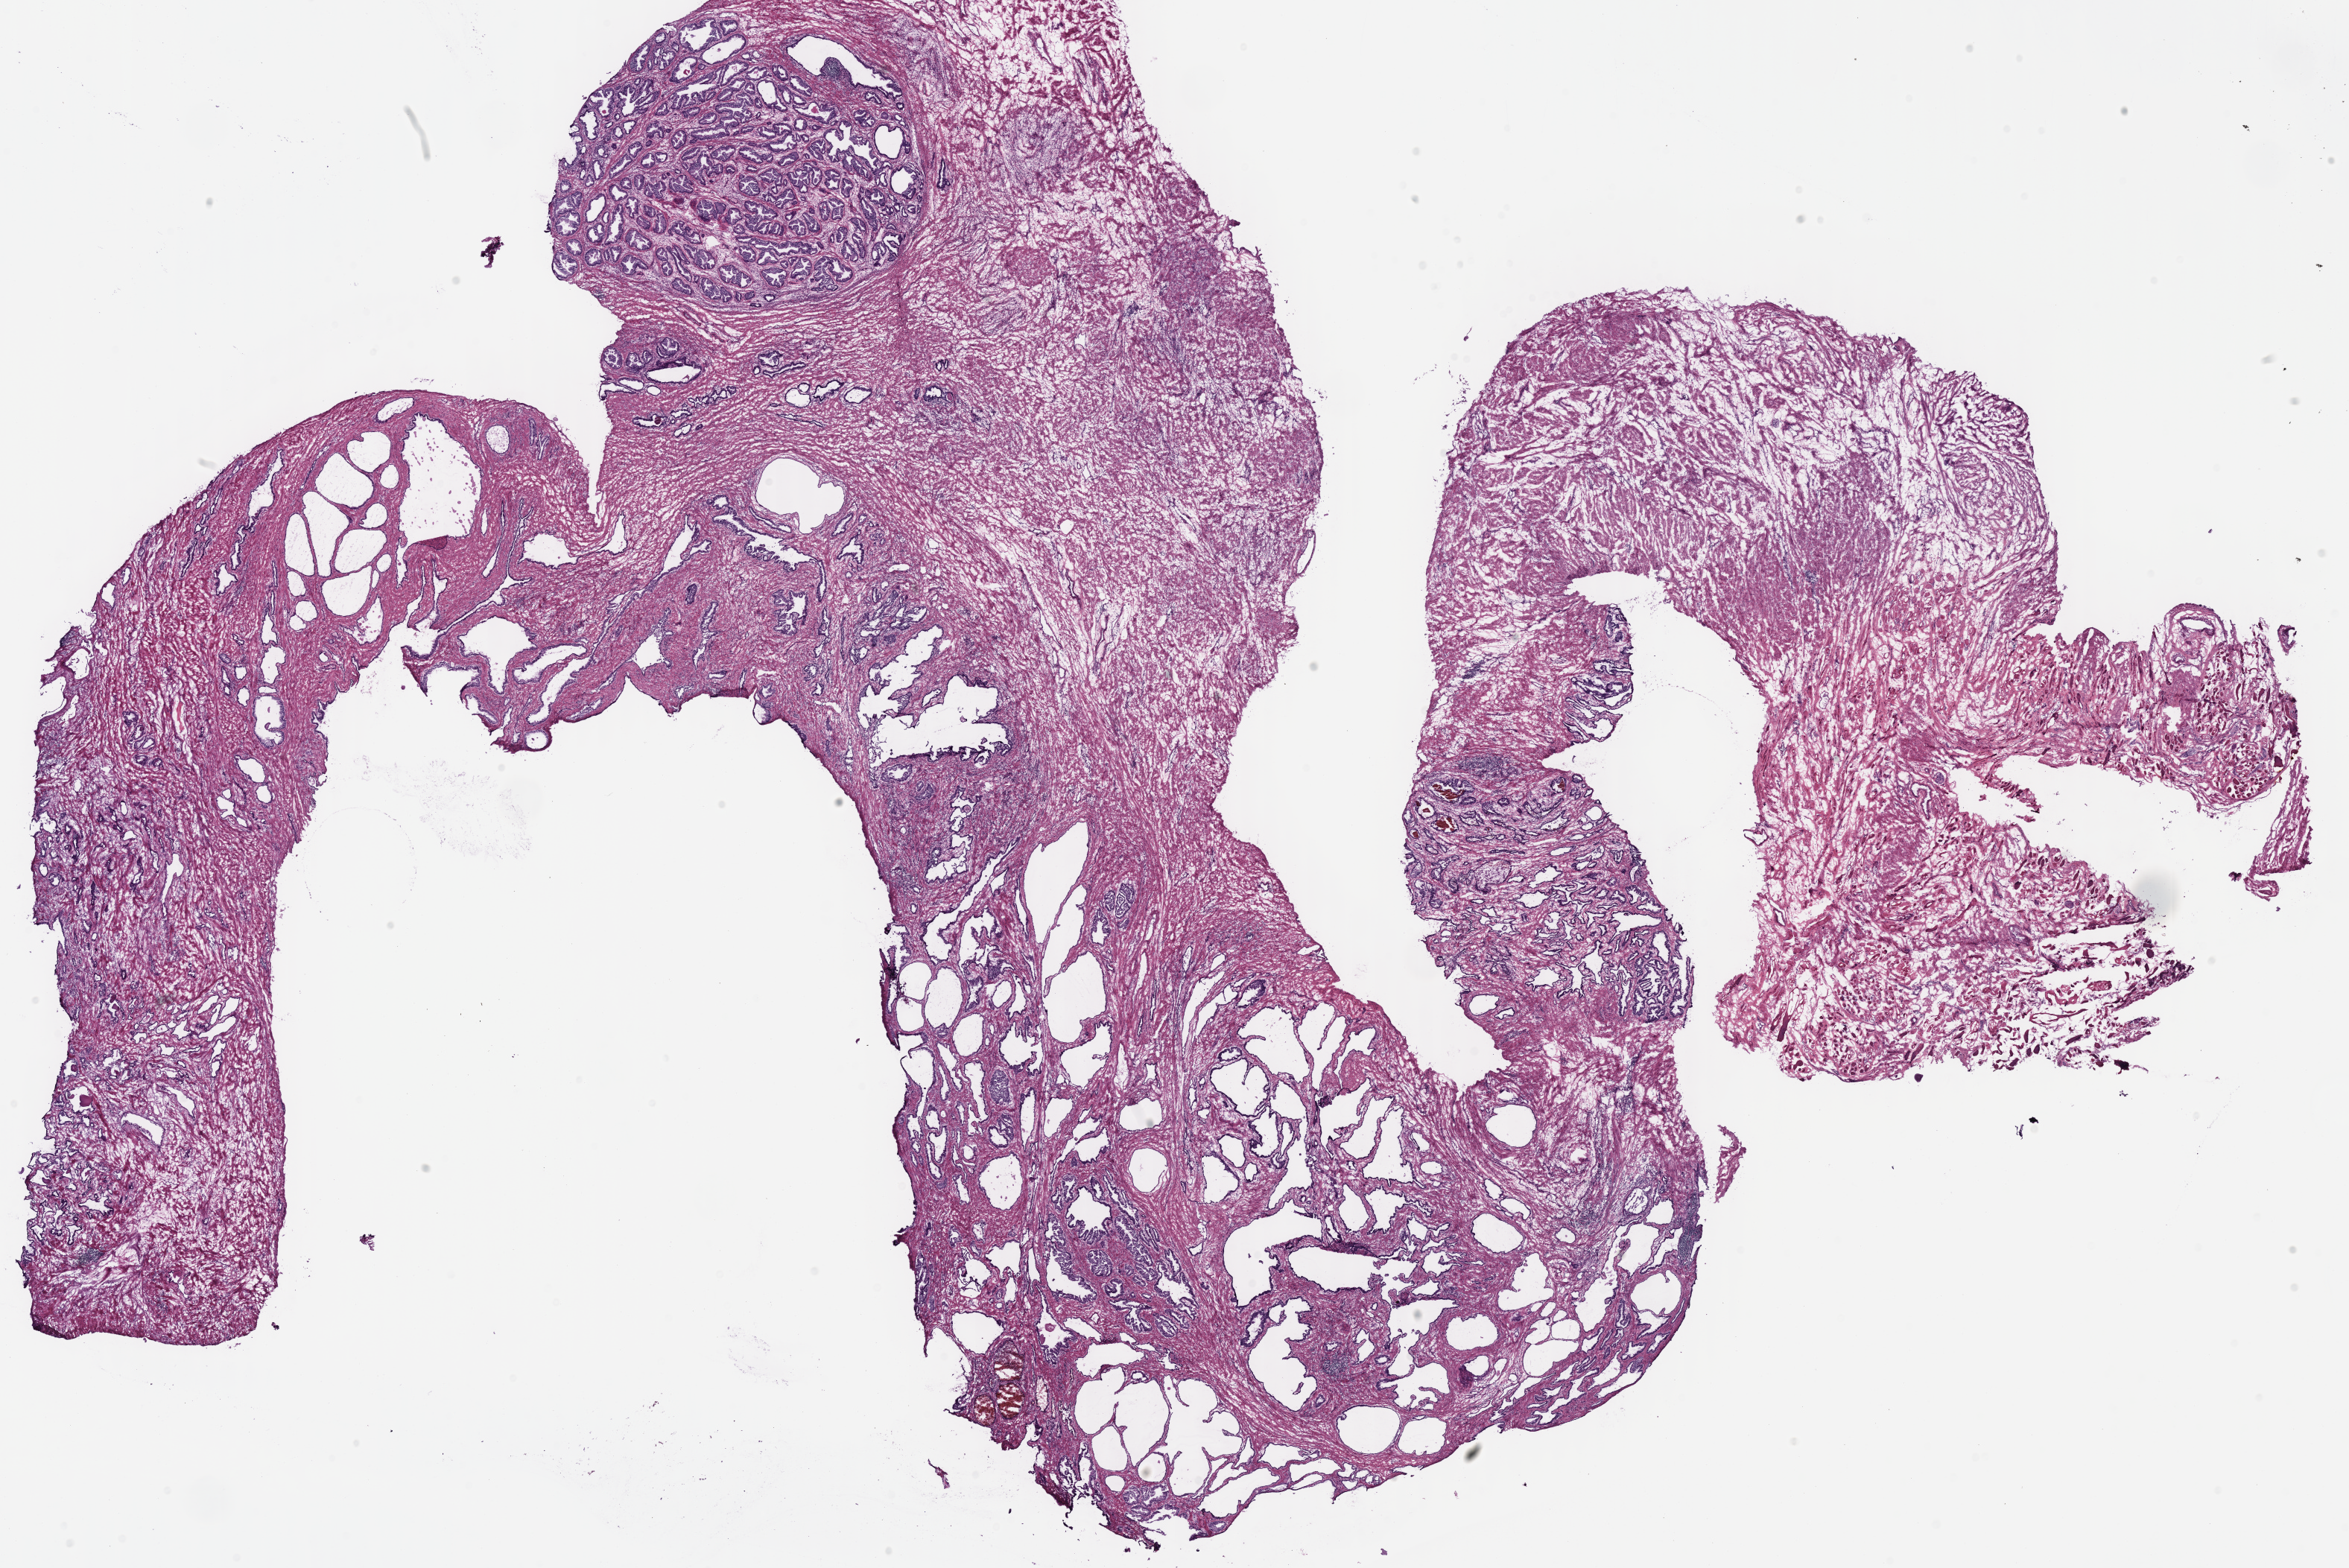
Digitized H&E tissue section (whole slide) — low-resolution overview of the scanned area, about 24.8 x 16.6 mm (acquisition: 40x scan), frozen section, sample: solid tissue normal (non-tumour tissue), prostate. Patient: male, age at initial diagnosis 64 years.
- this section: solid tissue normal (non-tumour) sample from the same patient
- patient diagnosis: Acinar cell carcinoma